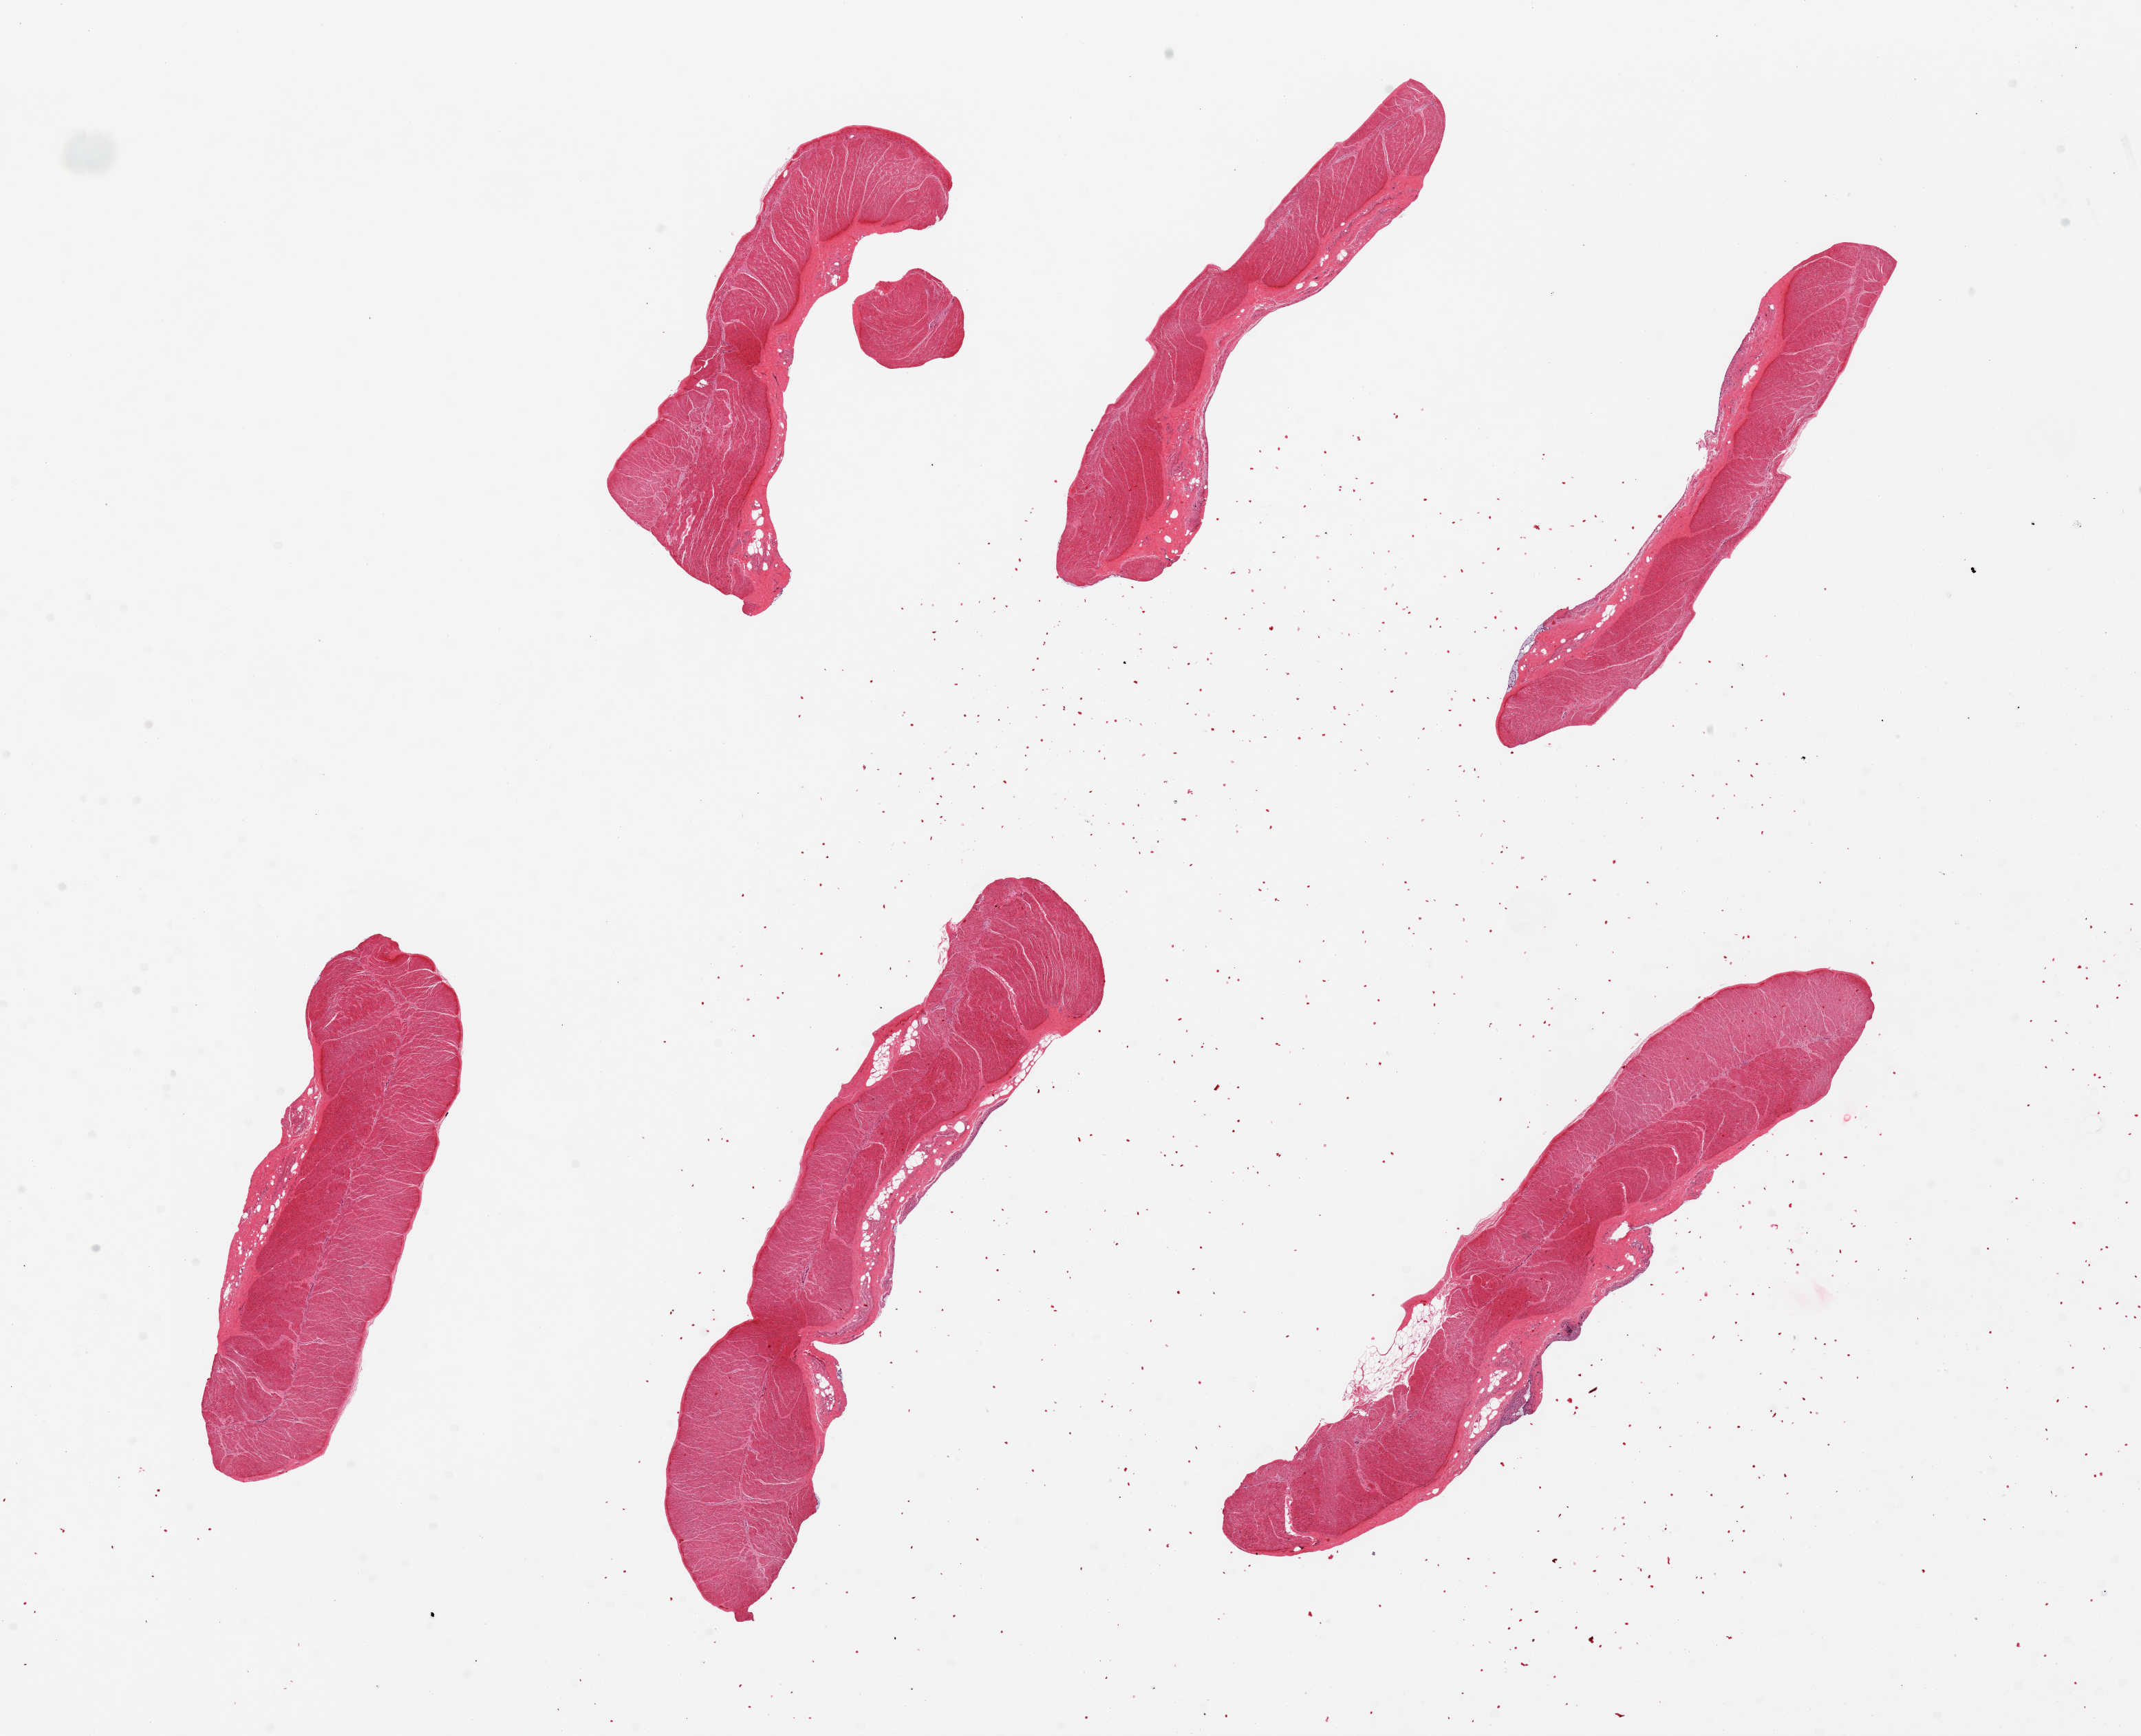
H&E whole-slide image, low-resolution overview of the scanned area, about 24.6 x 20.0 mm. PAXgene-fixed paraffin-embedded (PFPE) section. Section of sigmoid colon (target tissue). Donor tissue sample.
Reviewer comment on this tissue sample: 6 pieces.